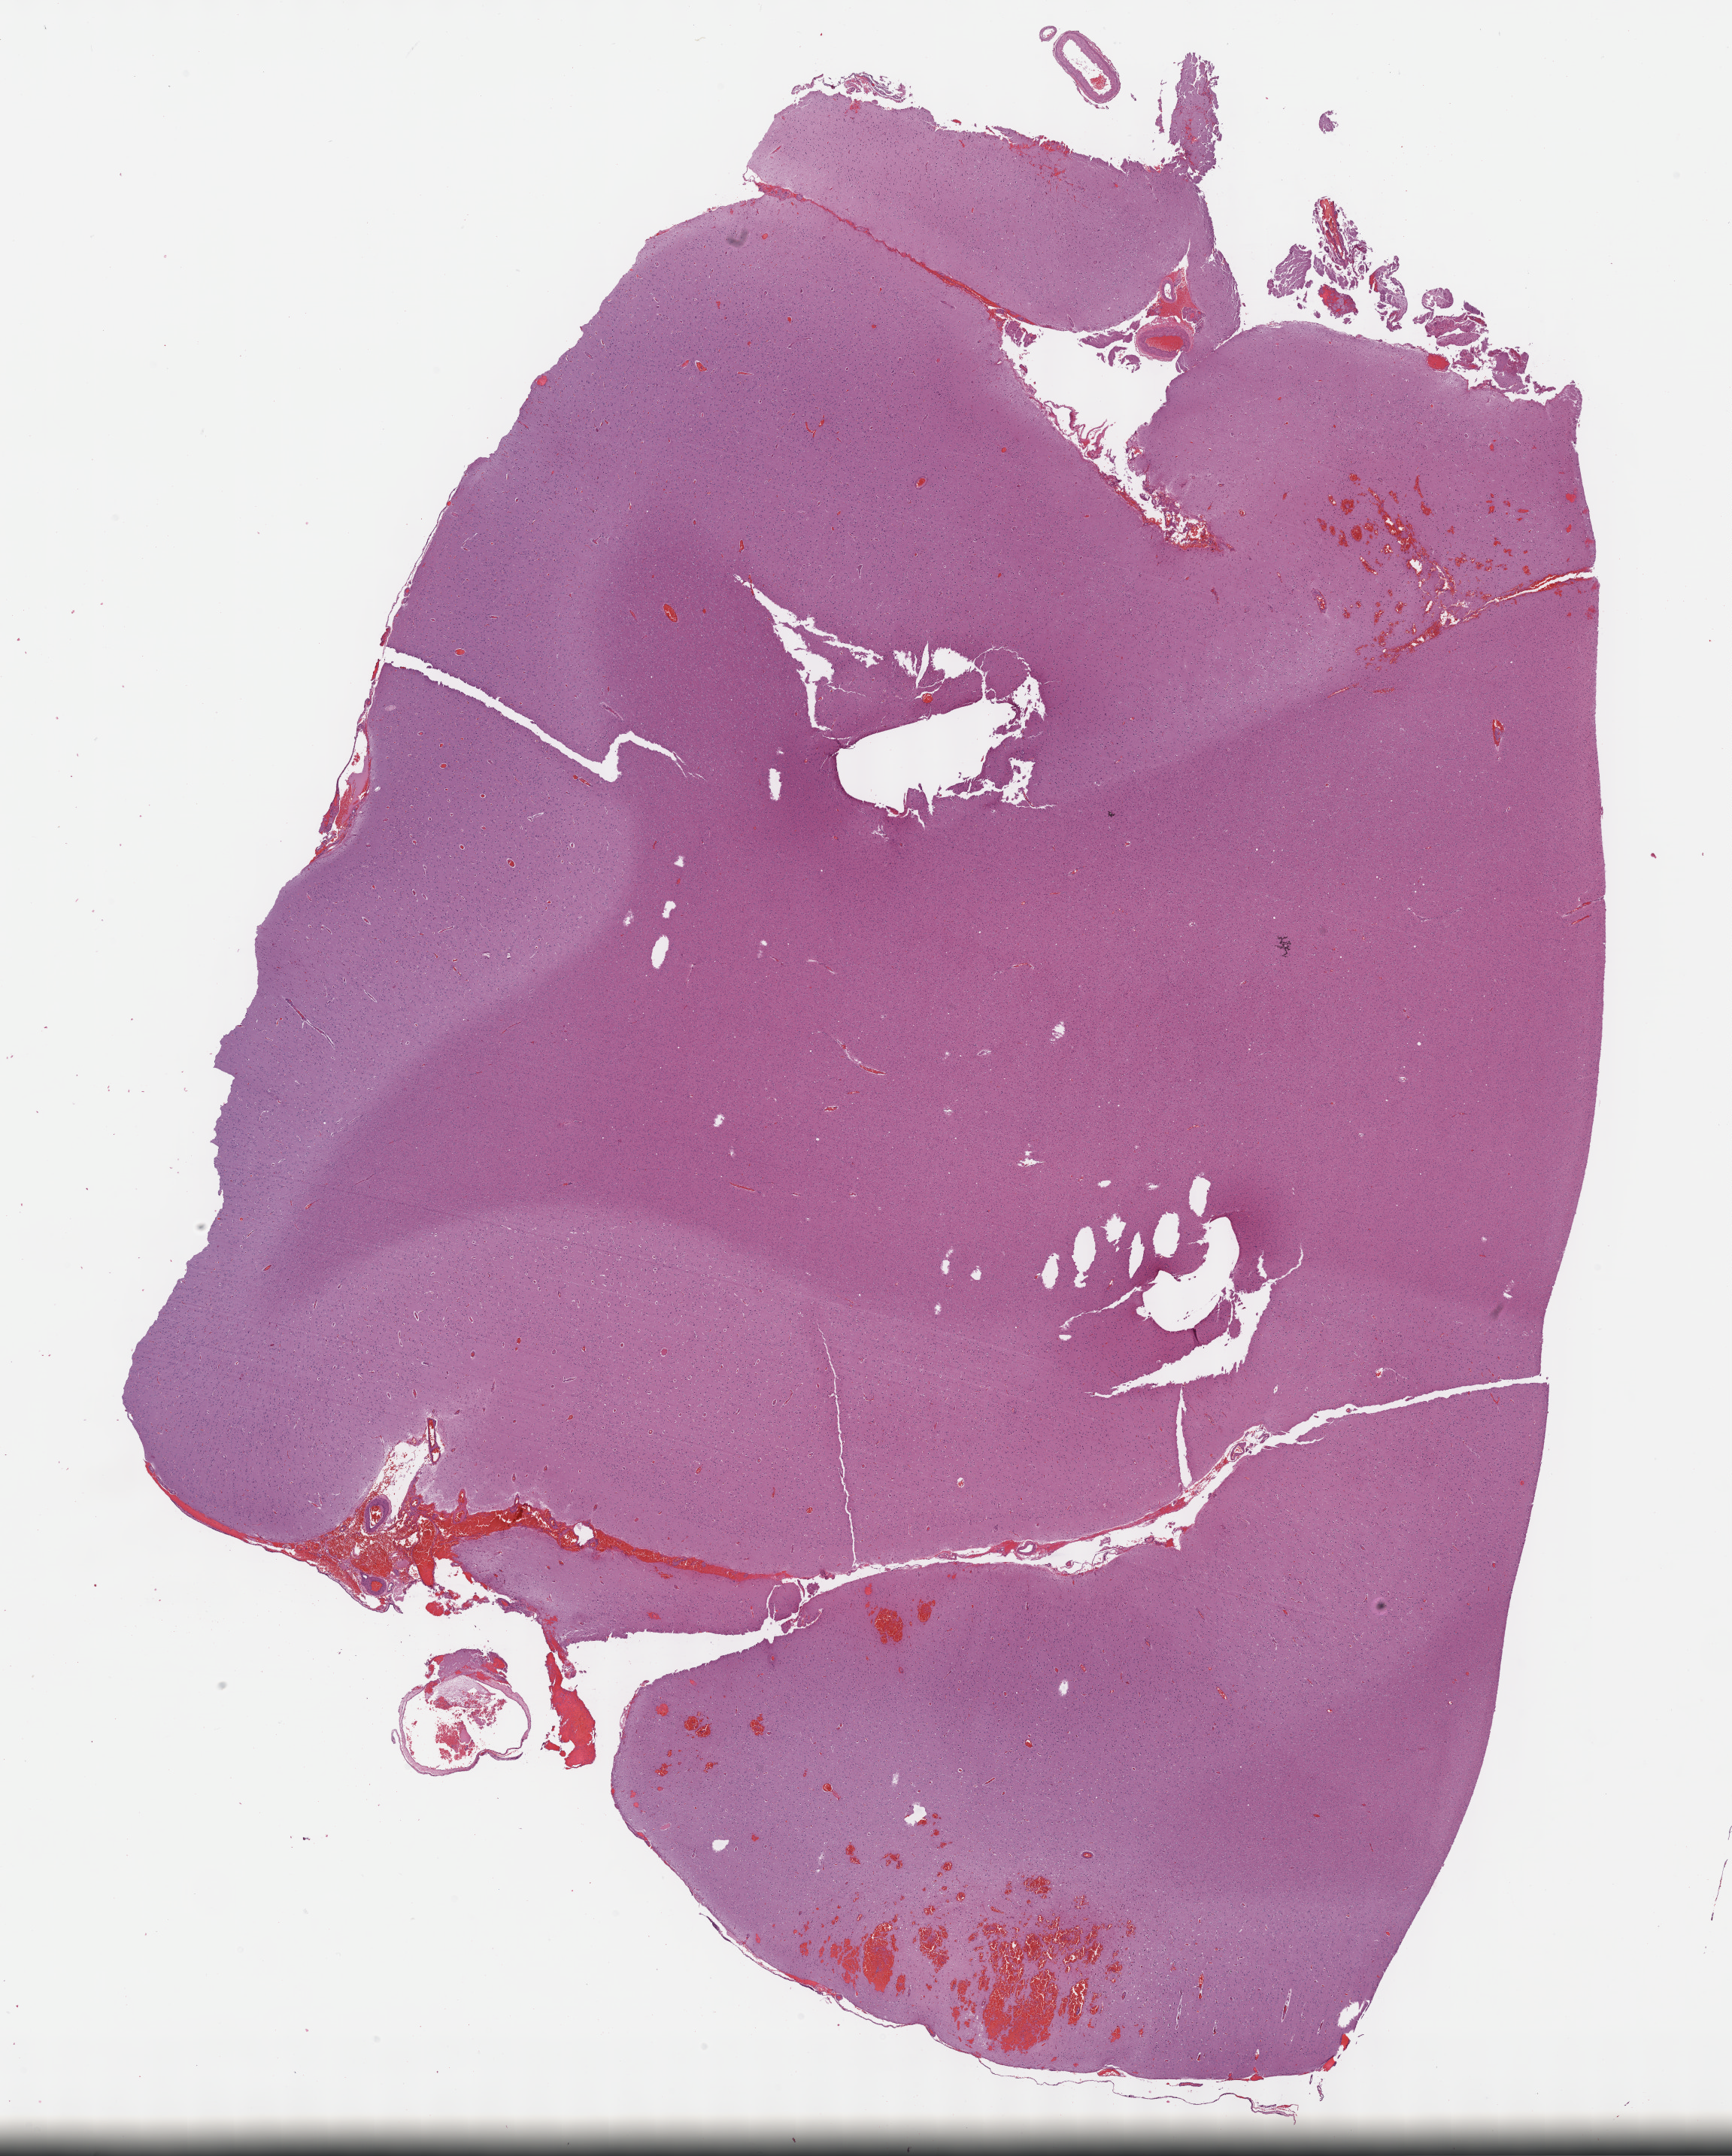
H&E-stained whole-slide image, whole scanned area (about 18.6 x 23.2 mm, acquisition: 40x scan) shown as a low-resolution overview; formalin-fixed paraffin-embedded (FFPE) diagnostic section; sample: primary tumour, brain. Male, age 61 years at initial diagnosis. Histologic grade: G2 (moderately differentiated).
Histologic diagnosis: Mixed glioma (cerebrum).